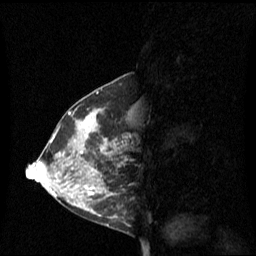
Breast MRI (dynamic contrast-enhanced), one sagittal slice. Position 29 of 60 along the scan axis. Dynamic contrast-enhanced series, image 2 of 3 at this slice position (ordered by acquisition). 1.5 T. TE 4.2 ms, TR 8.4 ms. 256 × 256 image matrix, field of view 240 × 240 mm. Female patient, age 42 years. Case-level facts recorded for this patient, not image findings: setting: breast cancer imaged before/during neoadjuvant chemotherapy; receptor status: HR-positive, HER2-negative.
Structures marked on this image (semi-automatic segmentation, software-assisted and operator-edited):
- analysis volume of interest (the breast-tissue region the enhancement analysis was run in; not a lesion): bounding box (x1, y1, x2, y2) in pixels: (68, 108, 131, 201)
- tumour enhancement mask (voxels above the 70 % enhancement threshold inside the analysis volume of interest): (84, 110, 117, 195)